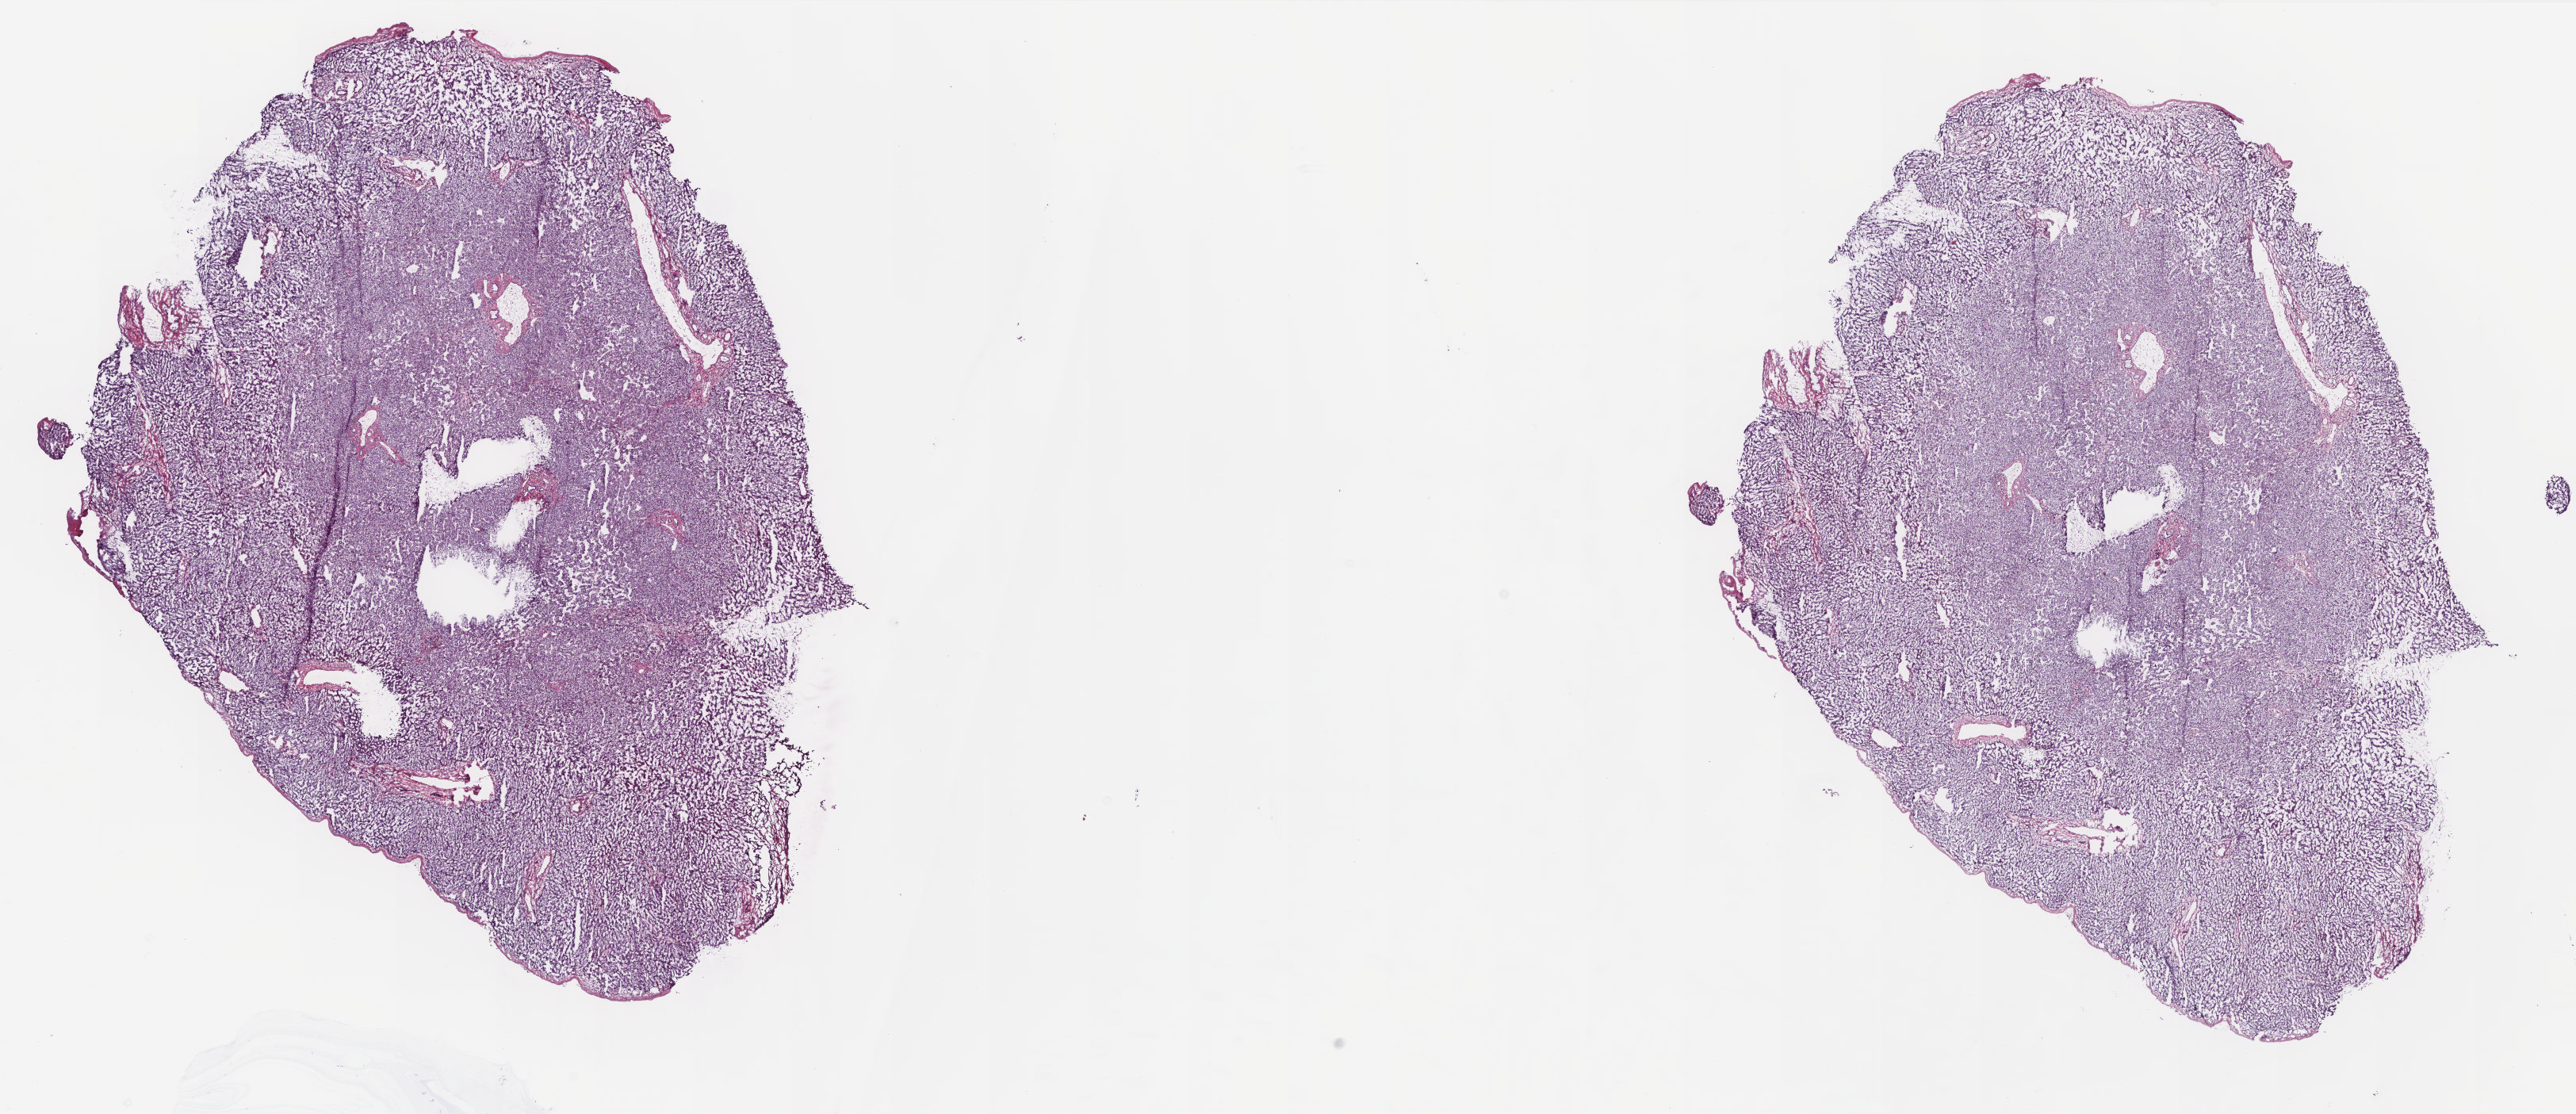
Whole-slide histology image, Hematoxylin and eosin (H&E) stained, a low-resolution overview of the entire scanned area, about 25.9 x 11.2 mm (slide scanned at 20x), frozen section, sample: solid tissue normal (non-tumour tissue), liver. Patient: male, age at initial diagnosis 73 years. Slide review estimates, as recorded: tumour cells 0%, tumour nuclei 0%, normal cells 80%, stromal cells 20%, necrosis 0%. Inflammatory infiltration, as recorded: lymphocyte infiltration 3%, monocyte infiltration 1%, neutrophil infiltration 1%.
- this section: solid tissue normal (non-tumour) sample from the same patient
- patient diagnosis: Hepatocellular carcinoma, NOS